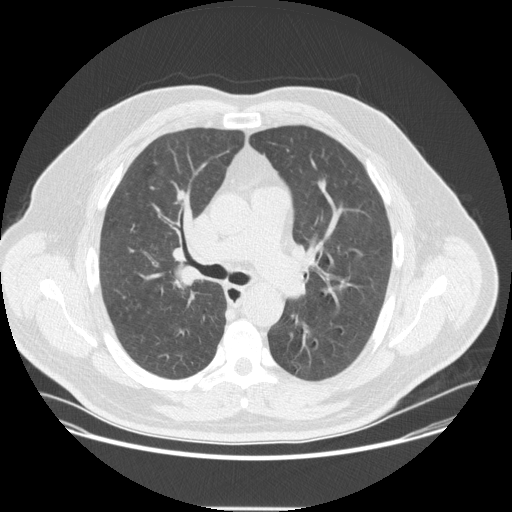
Low-dose screening chest CT, axial slice. Second annual screen. Lung window (W 1500 / L -600 HU). 512 × 512 image matrix. Male participant, aged 57 years at enrolment. Current smoker at enrolment.
- Lesion marked by an expert reader, bounding box <157,256,211,304> (left, top, right, bottom; pixels).
- Screening reader's record for this exam (one nodule recorded; not confirmed to be the boxed lesion): non-calcified nodule or mass ≥4 mm, right upper lobe, 20 × 16 mm, spiculated (stellate) margins, soft tissue attenuation, pre-existing on the prior screen: no.
- Official screen result: positive, other.